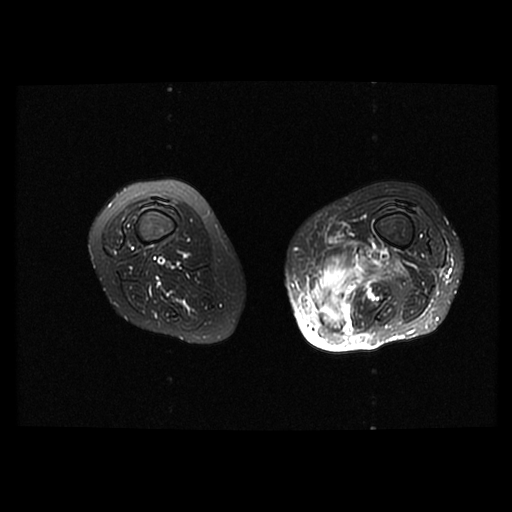
MRI of an extremity soft-tissue mass, one axial slice. Position 22 of 42 along the scan axis. T2-weighted fat-saturated. 6 mm slice thickness. 512 × 512 image matrix. Female patient. From the clinical record (not read from this slice): histological type: pleomorphic leiomyosarcoma; grade: high; site of the primary tumour: left thigh.
Structures marked on this image (expert manual segmentation):
- gross tumour volume including surrounding oedema: bounding box (x1, y1, x2, y2) in pixels: (309, 247, 395, 334)